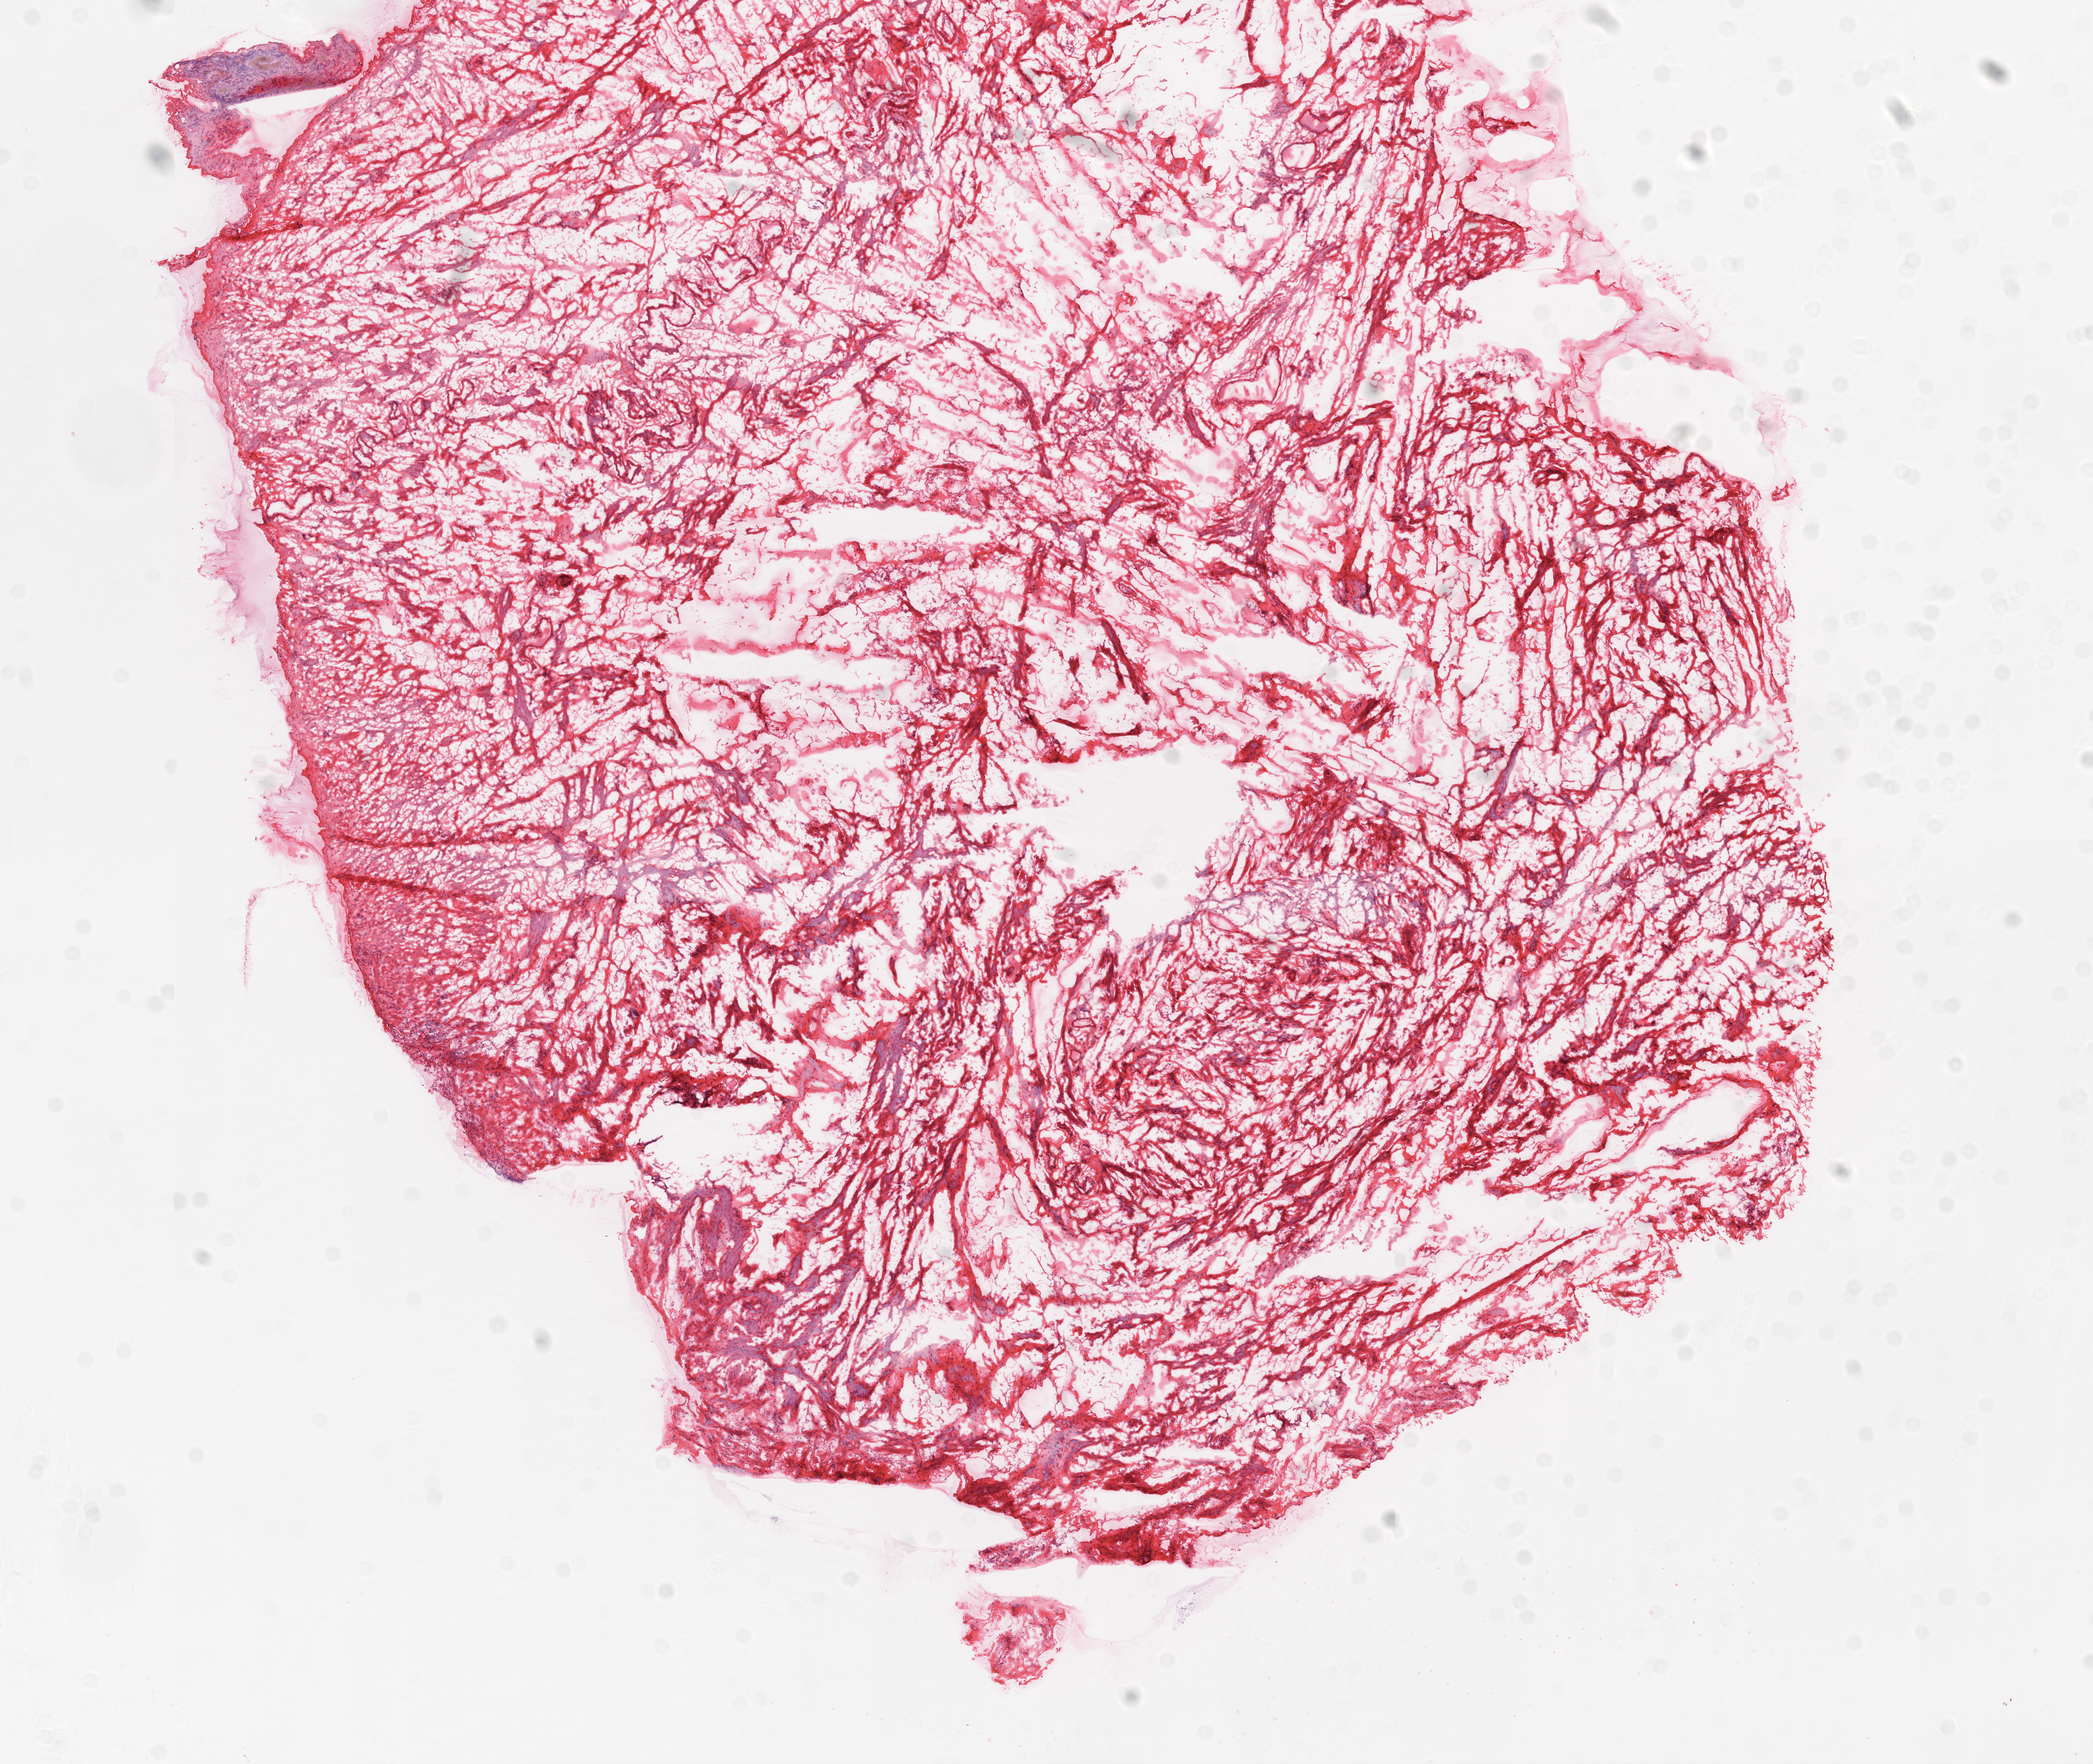
Whole-slide histology image, H&E — shown as a low-resolution overview of the whole scanned area (about 12.0 x 10.1 mm, slide scanned at 20x). Frozen section. Sample: solid tissue normal (non-tumour tissue), ovary. Female patient; age at initial diagnosis 57 years.
This section: solid tissue normal (non-tumour) sample from the same patient. Patient diagnosis: Serous cystadenocarcinoma, NOS.